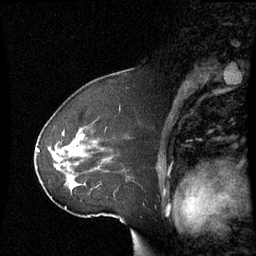
Breast MRI (dynamic contrast-enhanced), one sagittal slice; slice 41 of 60 in the series (ordered by position); dynamic contrast-enhanced series, image 2 of 3 at this slice position (ordered by acquisition); 1.5 T; TE 4.2 ms, TR 8.9 ms; 2.4 mm slice thickness; 256 × 256 image matrix, field of view 230 × 230 mm. Patient: female, 51 years. From the clinical record (not read from this slice): setting: breast cancer imaged before/during neoadjuvant chemotherapy; receptor status: HR-positive, HER2-negative.
Structures marked on this image (semi-automatically segmented with operator editing):
- analysis volume of interest (the breast-tissue region the enhancement analysis was run in; not a lesion): box from (x=42, y=124) to (x=111, y=199) px
- tumour enhancement mask (voxels above the 70 % enhancement threshold inside the analysis volume of interest): (x=74, y=135)–(x=84, y=145)